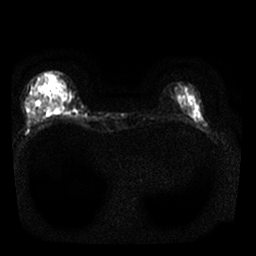
Breast MRI, one axial slice. Position 6 of 25 along the scan axis. Diffusion-weighted series; image 2 of 4 stored at this slice position (different b-values; order by instance number). 1.5 T. 4 mm slice thickness. 256 × 256 image matrix, field of view 310 × 310 mm. Female patient.
Outlined on this slice (manually delineated by an expert):
- tumour on diffusion-weighted imaging: box from (x=57, y=91) to (x=65, y=100) px